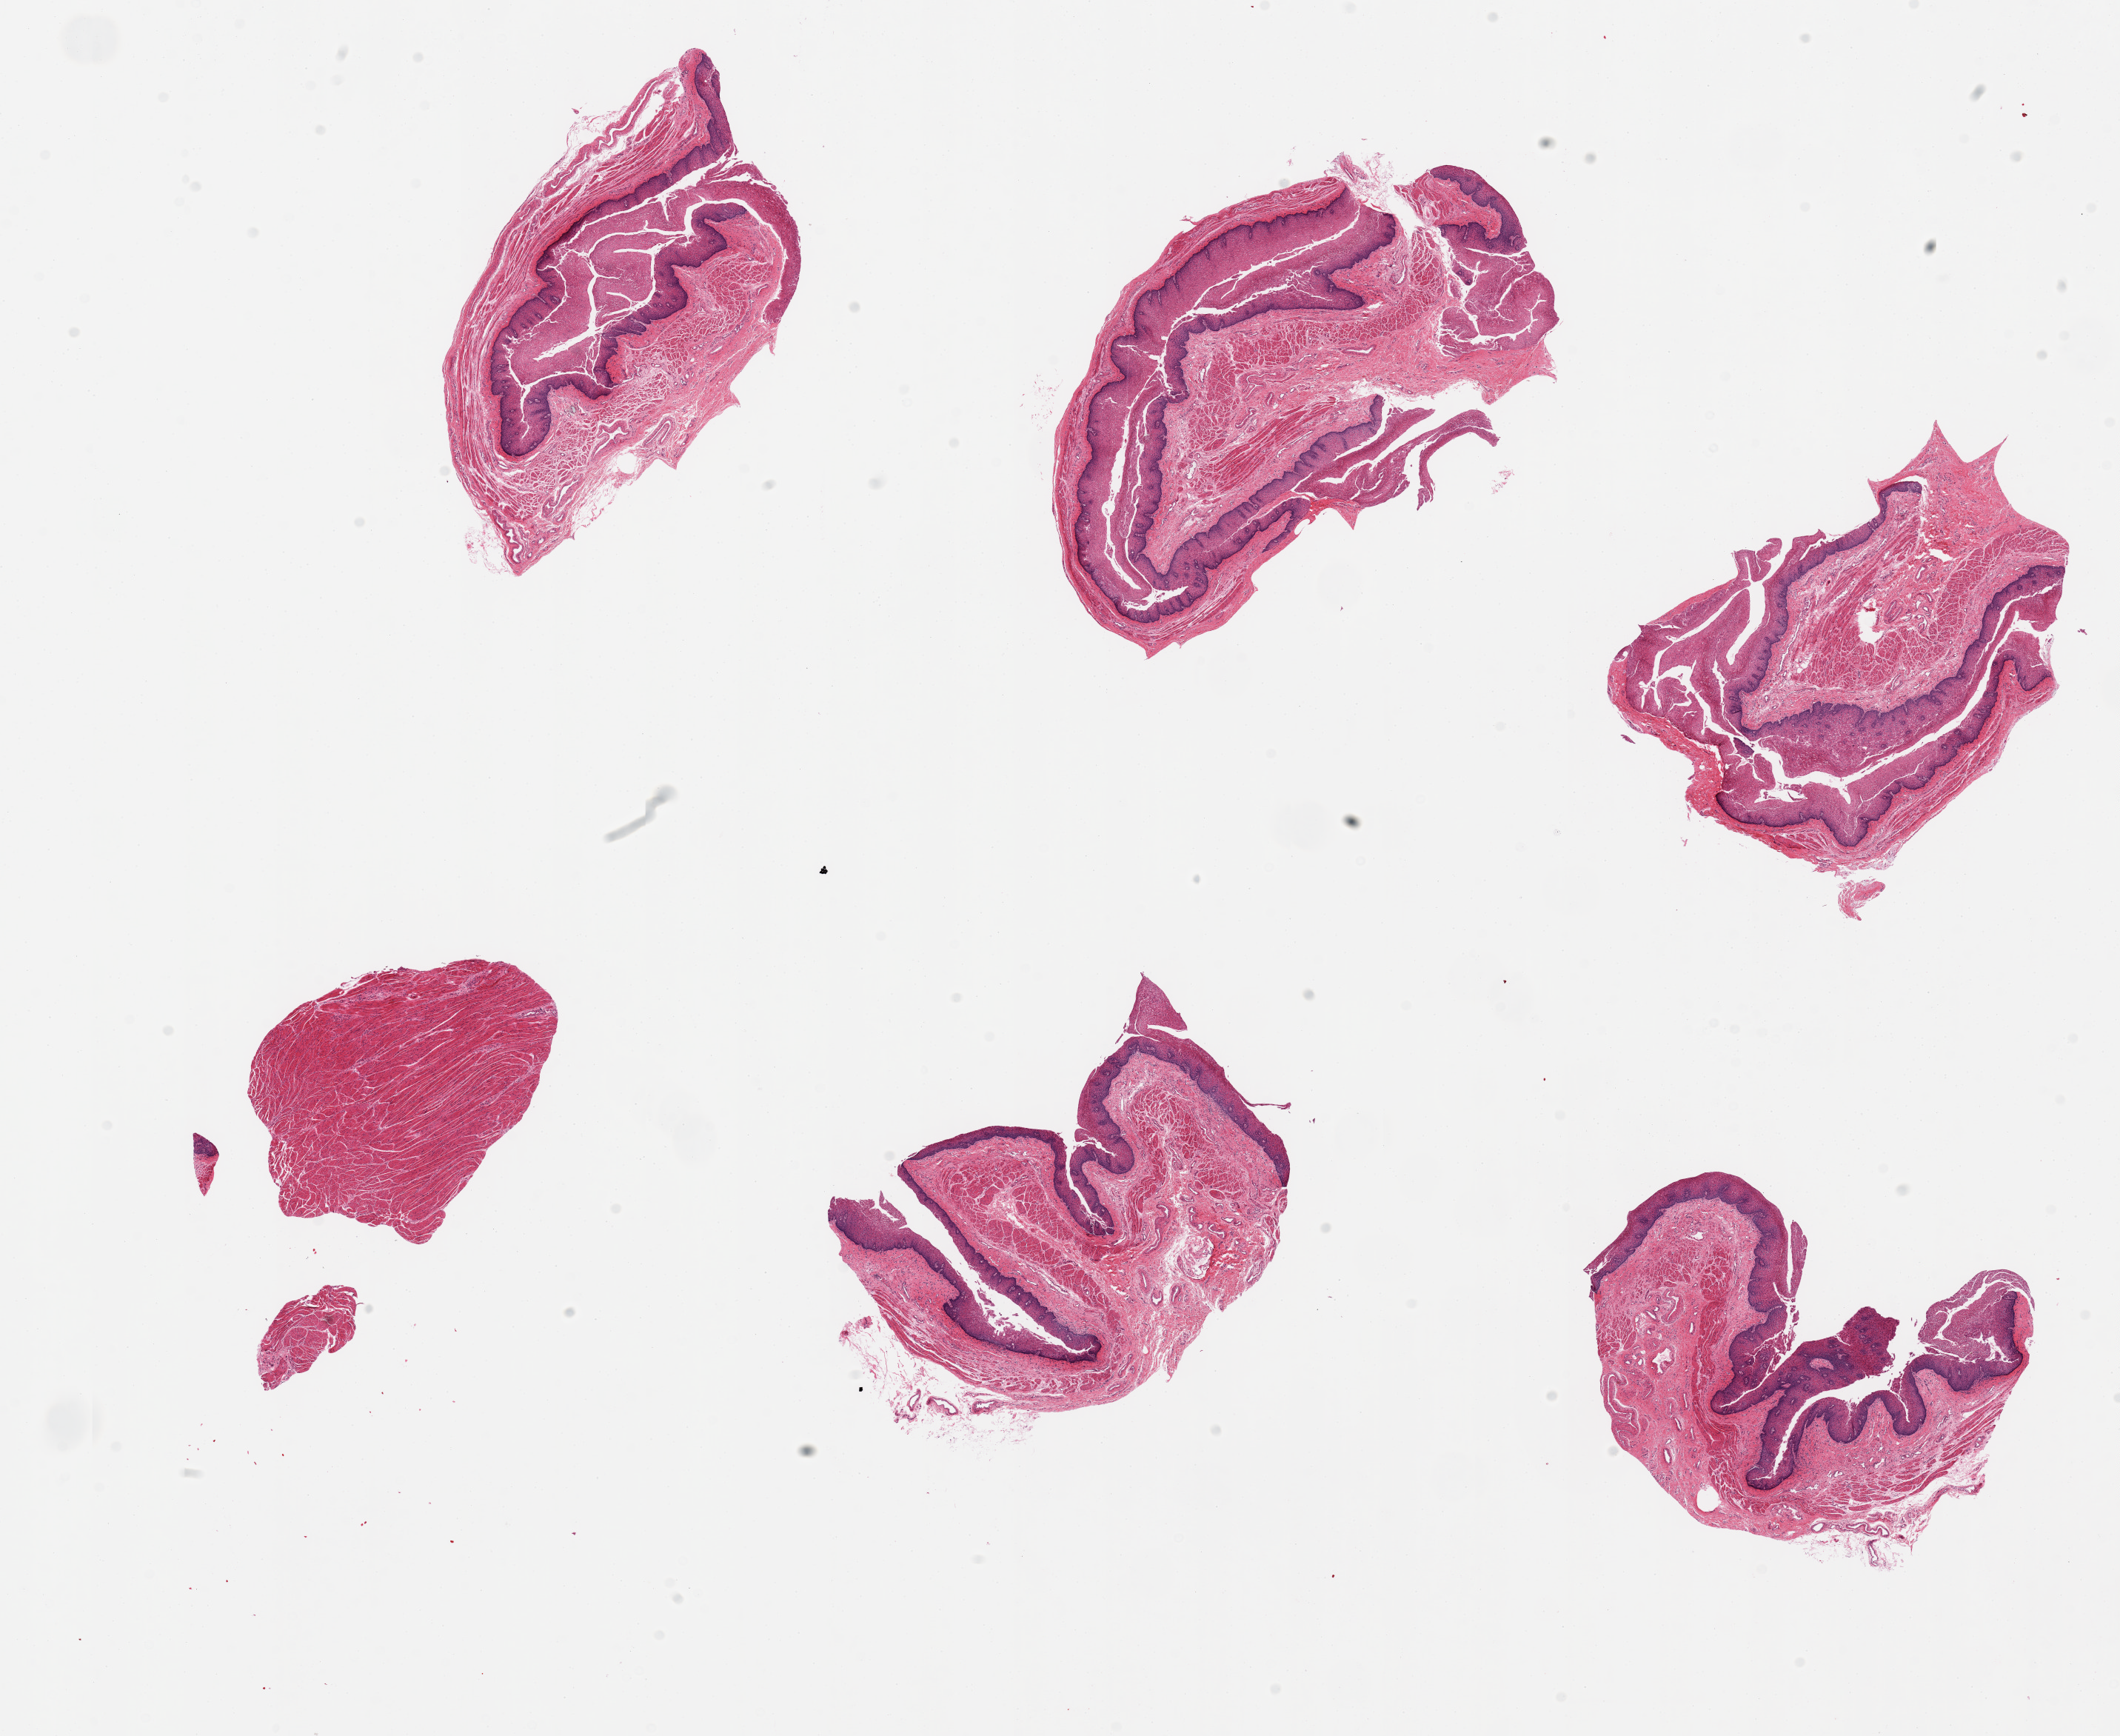
Whole-slide image, haematoxylin and eosin stain — low-resolution overview of the scanned area, about 22.6 x 18.5 mm (acquisition: 20x scan); PAXgene-fixed paraffin-embedded (PFPE) section; section of esophageal mucous membrane (target tissue); tissue donor sample. Donor: female.
• pathologist's review note for this sample: 6 pieces, 5 include squamous epithelium and muscularis mucosae, one piece is all muscle